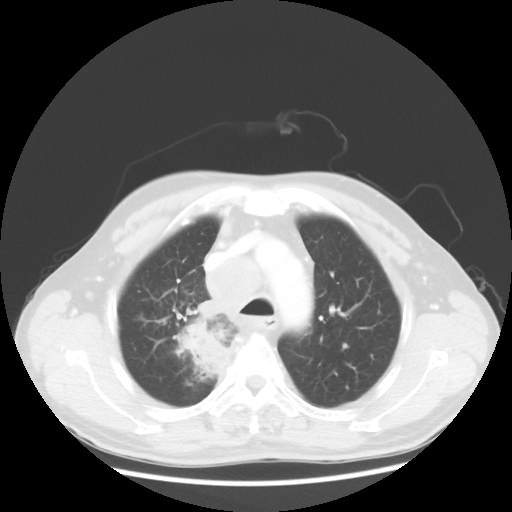
Chest CT, one axial slice. Slice 93 of 124 in the series (ordered by position). Reconstruction kernel STANDARD. 100 kVp. Lung window (W 1500 / L -600 HU). 512 × 512 image matrix. Male patient, age 64 years. Case-level facts recorded for this patient, not image findings: clinical TNM (as recorded): T3 N3 M0; histopathological grade: G3.
Structures marked on this image (bounding box drawn by a radiologist):
- lung tumour (recorded histology: small cell carcinoma): bounding box <179,300,233,393> (left, top, right, bottom; pixels)